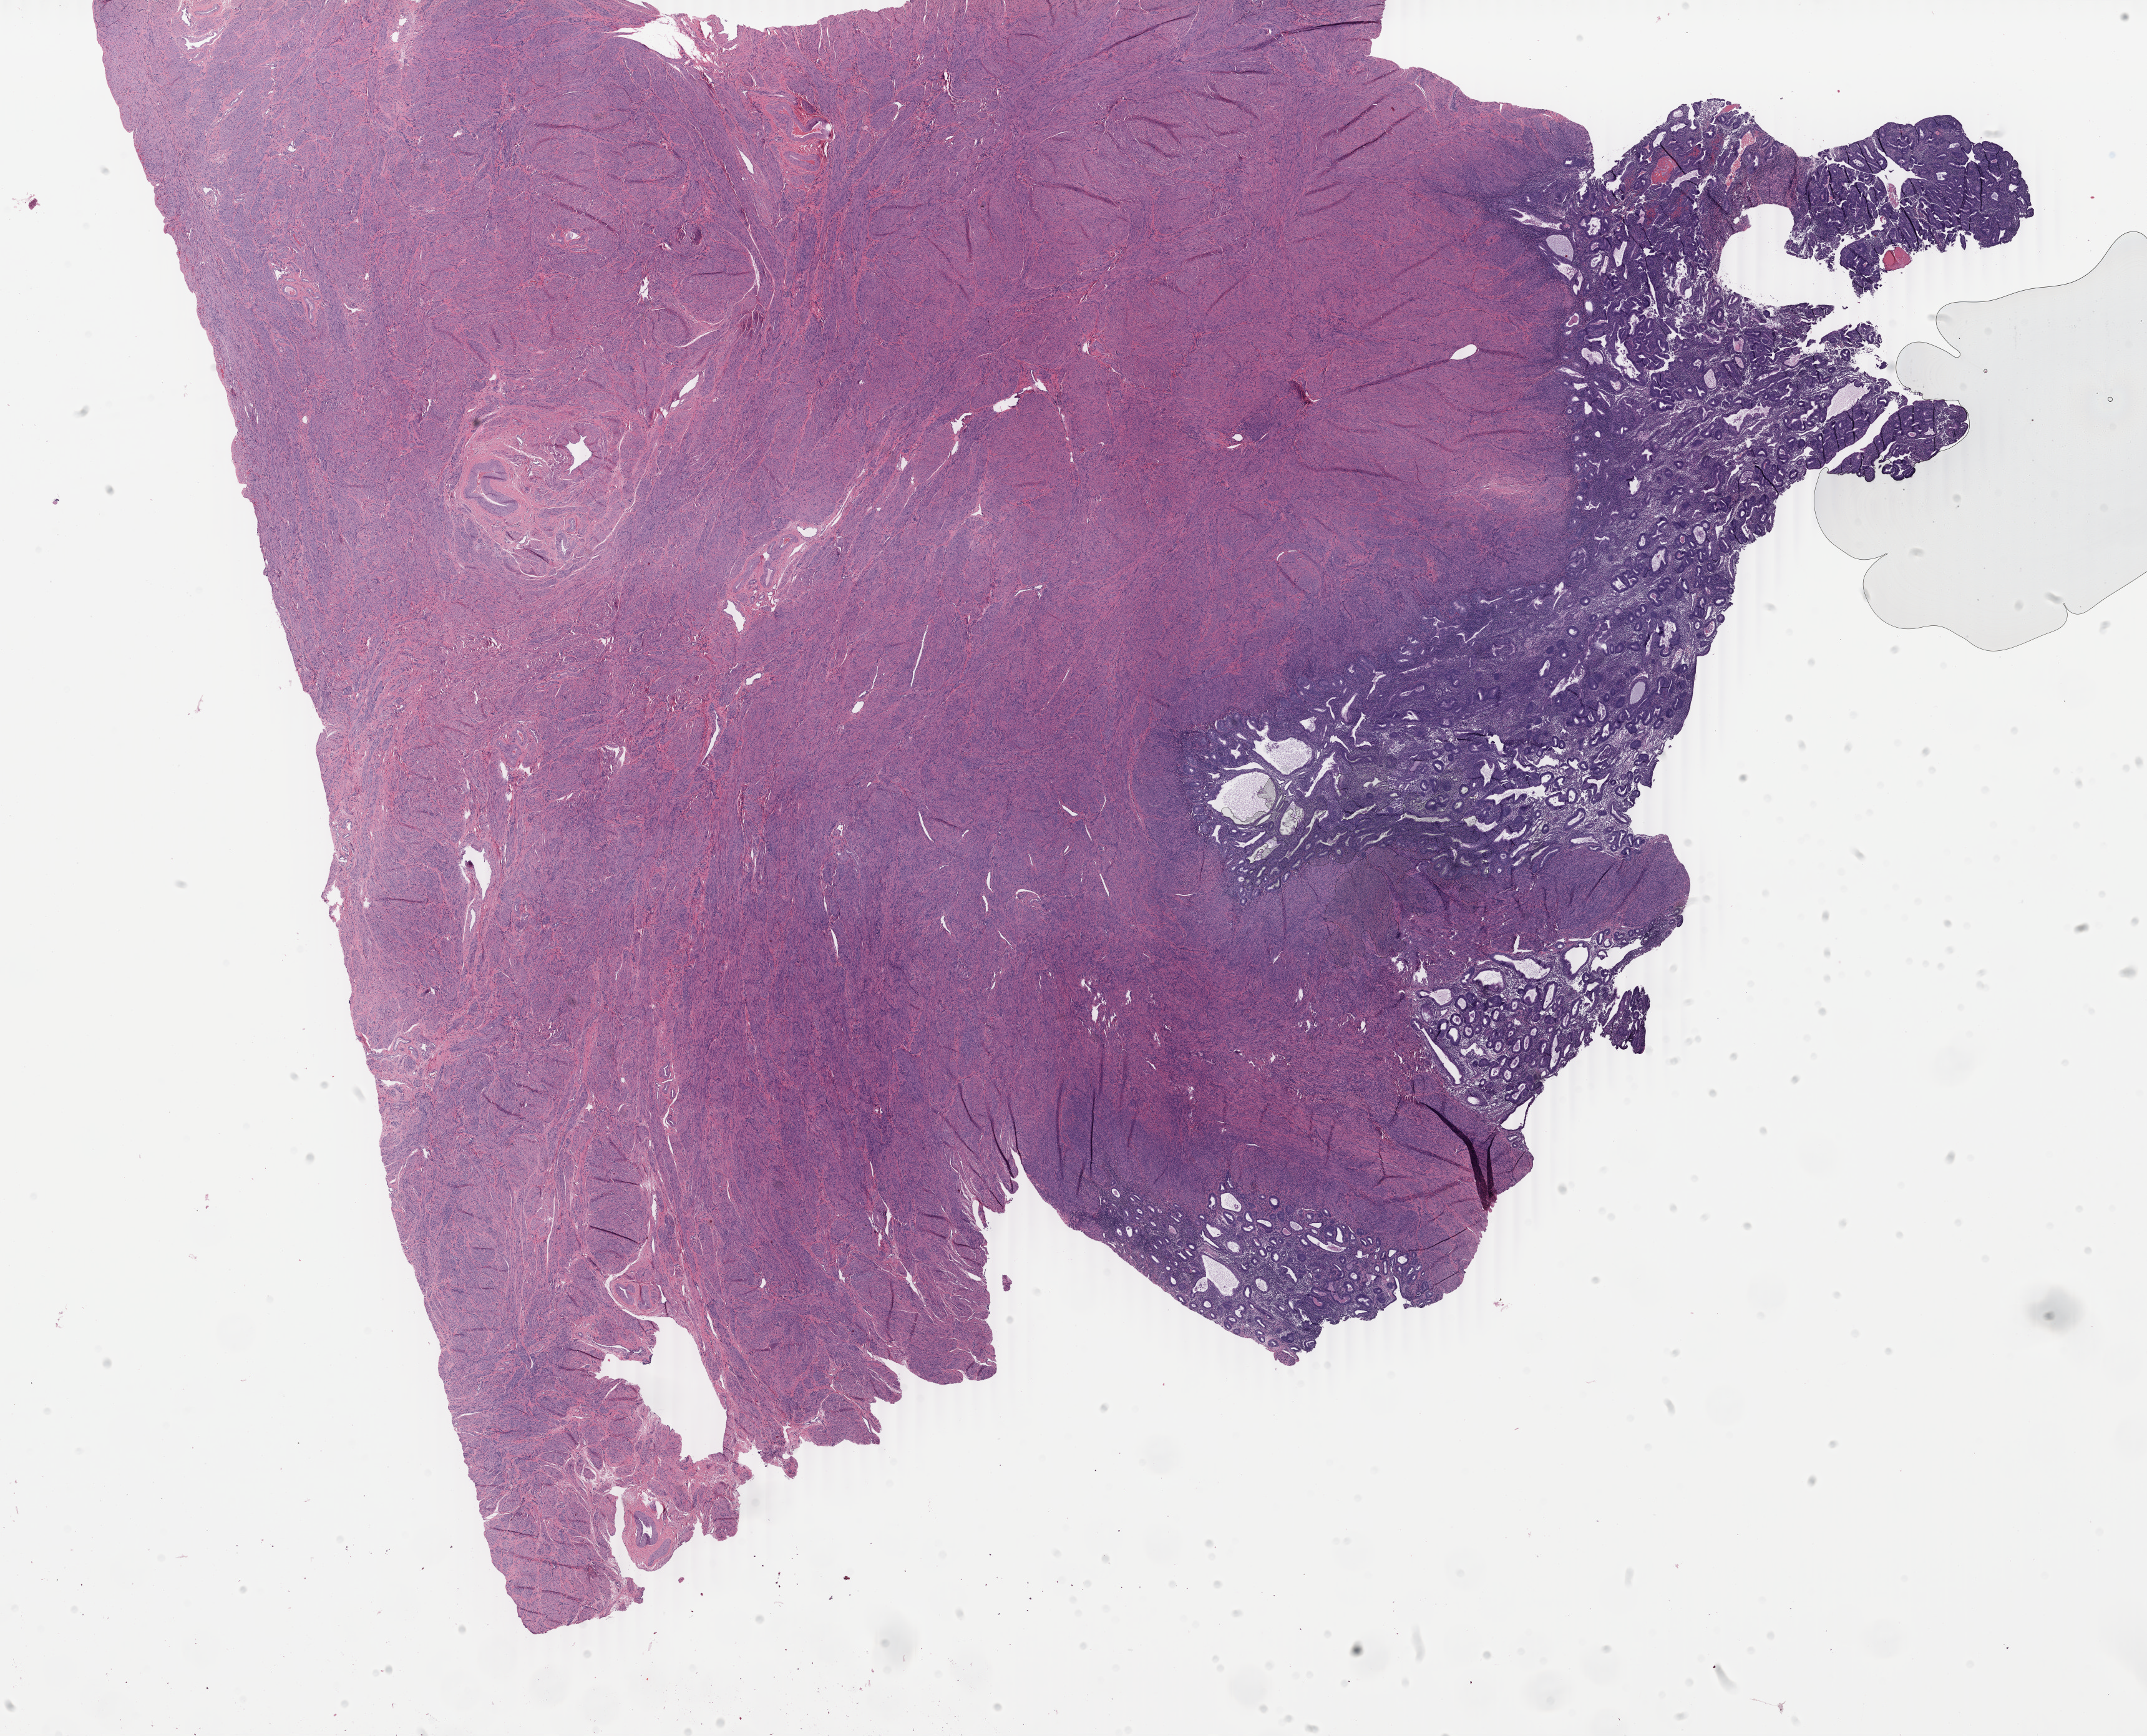
Whole-slide histology image, H&E-stained — low-resolution overview of the scanned area, about 27.4 x 22.1 mm (slide scanned at 40x); formalin-fixed paraffin-embedded (FFPE) diagnostic section; primary tumour sample from the uterus. Patient: female, age at initial diagnosis 58 years. Histologic grade: G1 (well differentiated).
- FIGO stage: IB
- pathologic diagnosis: Endometrioid adenocarcinoma, NOS (endometrium)